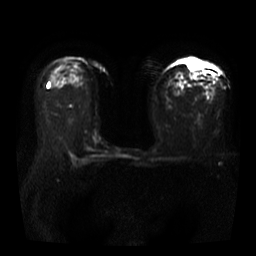
Breast MRI, one axial slice; diffusion-weighted series; image 2 of 4 stored at this slice position (different b-values; order by instance number); 3 T; 256 × 256 image matrix. Female patient.
Outlined on this slice (manually delineated by an expert):
- tumour on diffusion-weighted imaging: box from (x=187, y=60) to (x=199, y=71) px